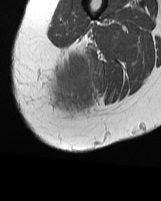
MRI of an extremity soft-tissue mass, one axial slice. Position 14 of 70 along the scan axis. MR volume resampled by the dataset authors to the PET/CT grid (not the native acquisition matrix). 3.27 mm slice thickness. 161 × 201 image matrix. Female patient. From the clinical record (not read from this slice): histological type: synovial sarcoma; grade: intermediate; site of the primary tumour: right buttock.
Structures marked on this image (expert contour drawn on MRI and transferred to this co-registered scan by the dataset authors):
- gross tumour volume including surrounding oedema: box from (x=54, y=47) to (x=96, y=110) px
- gross tumour volume (mass): (x=54, y=59)–(x=96, y=109)